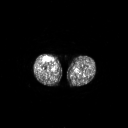
FDG PET of an extremity soft-tissue mass (from a PET/CT study), one axial slice. 128 × 128 image matrix, field of view 700 × 700 mm. Male patient, age 56 years. Case-level facts recorded for this patient, not image findings: histological type: pleiomorphic leiomyosarcoma; grade: intermediate; site of the primary tumour: right thigh.
Annotated regions visible in this slice (expert contour drawn on MRI and transferred to this co-registered scan by the dataset authors):
- gross tumour volume including surrounding oedema: bounding box <43,56,51,62> (left, top, right, bottom; pixels)